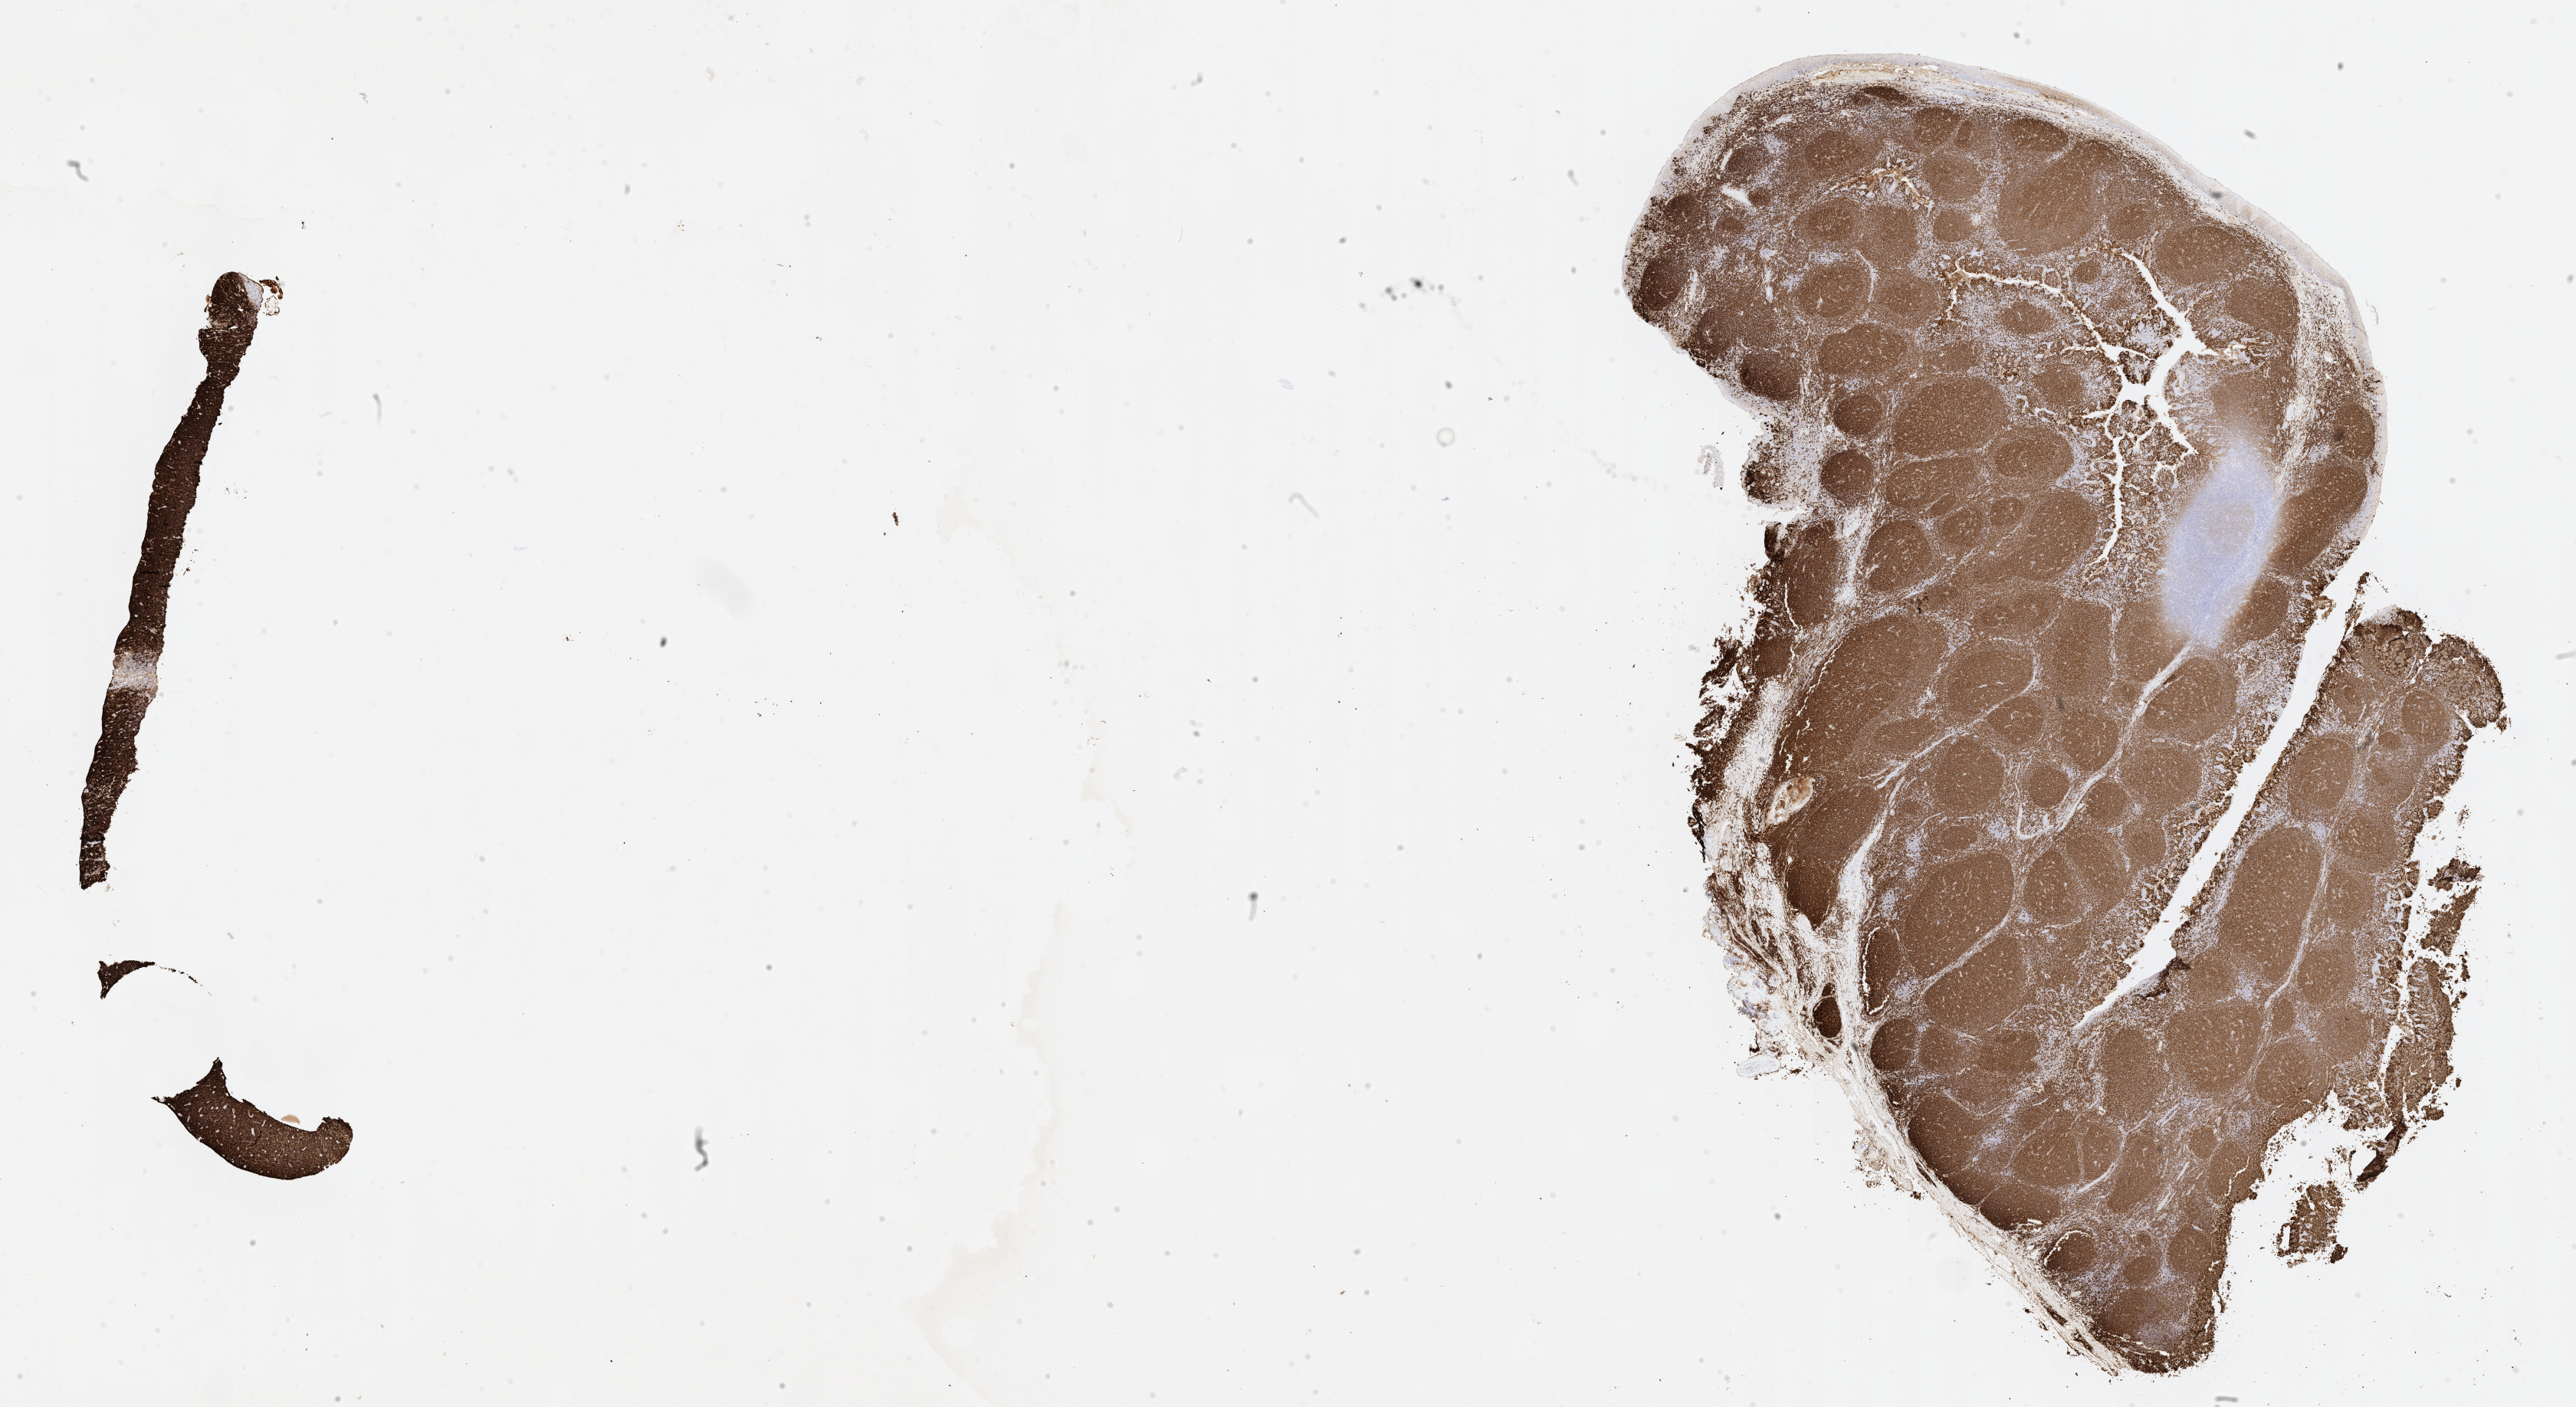
Immunohistochemistry (IHC) whole-slide image stained for CD20 — whole scanned area (about 27.2 x 14.8 mm) shown as a low-resolution overview; tumor tissue; anatomic site: ovary. Female patient; age at initial diagnosis 9 years.
• diagnosis: Burkitt lymphoma, NOS